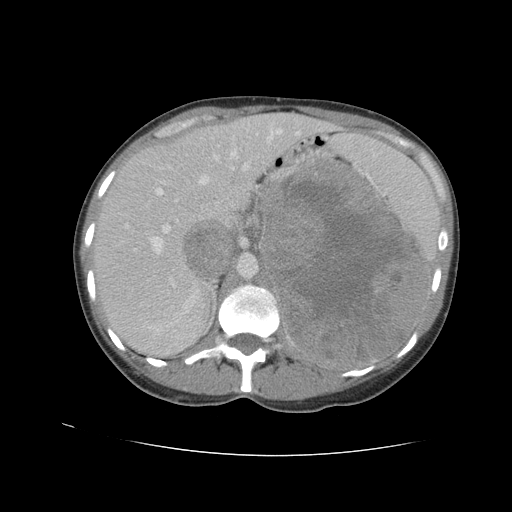
Contrast-enhanced abdominal CT, one axial slice; slice 69 of 90 in the series (ordered by position); reconstruction kernel STANDARD; soft-tissue window (W 400 / L 40 HU); 5 mm slice thickness; 512 × 512 image matrix, field of view 360 × 360 mm. Female patient. Case-level facts recorded for this patient, not image findings: diagnosis: adrenocortical carcinoma; tumour side: left adrenal; tumour size at pathology: 18 cm; Ki-67 index: 11 %.
Annotated regions visible in this slice (semi-automatic segmentation, software-assisted and operator-edited):
- mass: bounding box (x1, y1, x2, y2) in pixels: (261, 160, 428, 368)